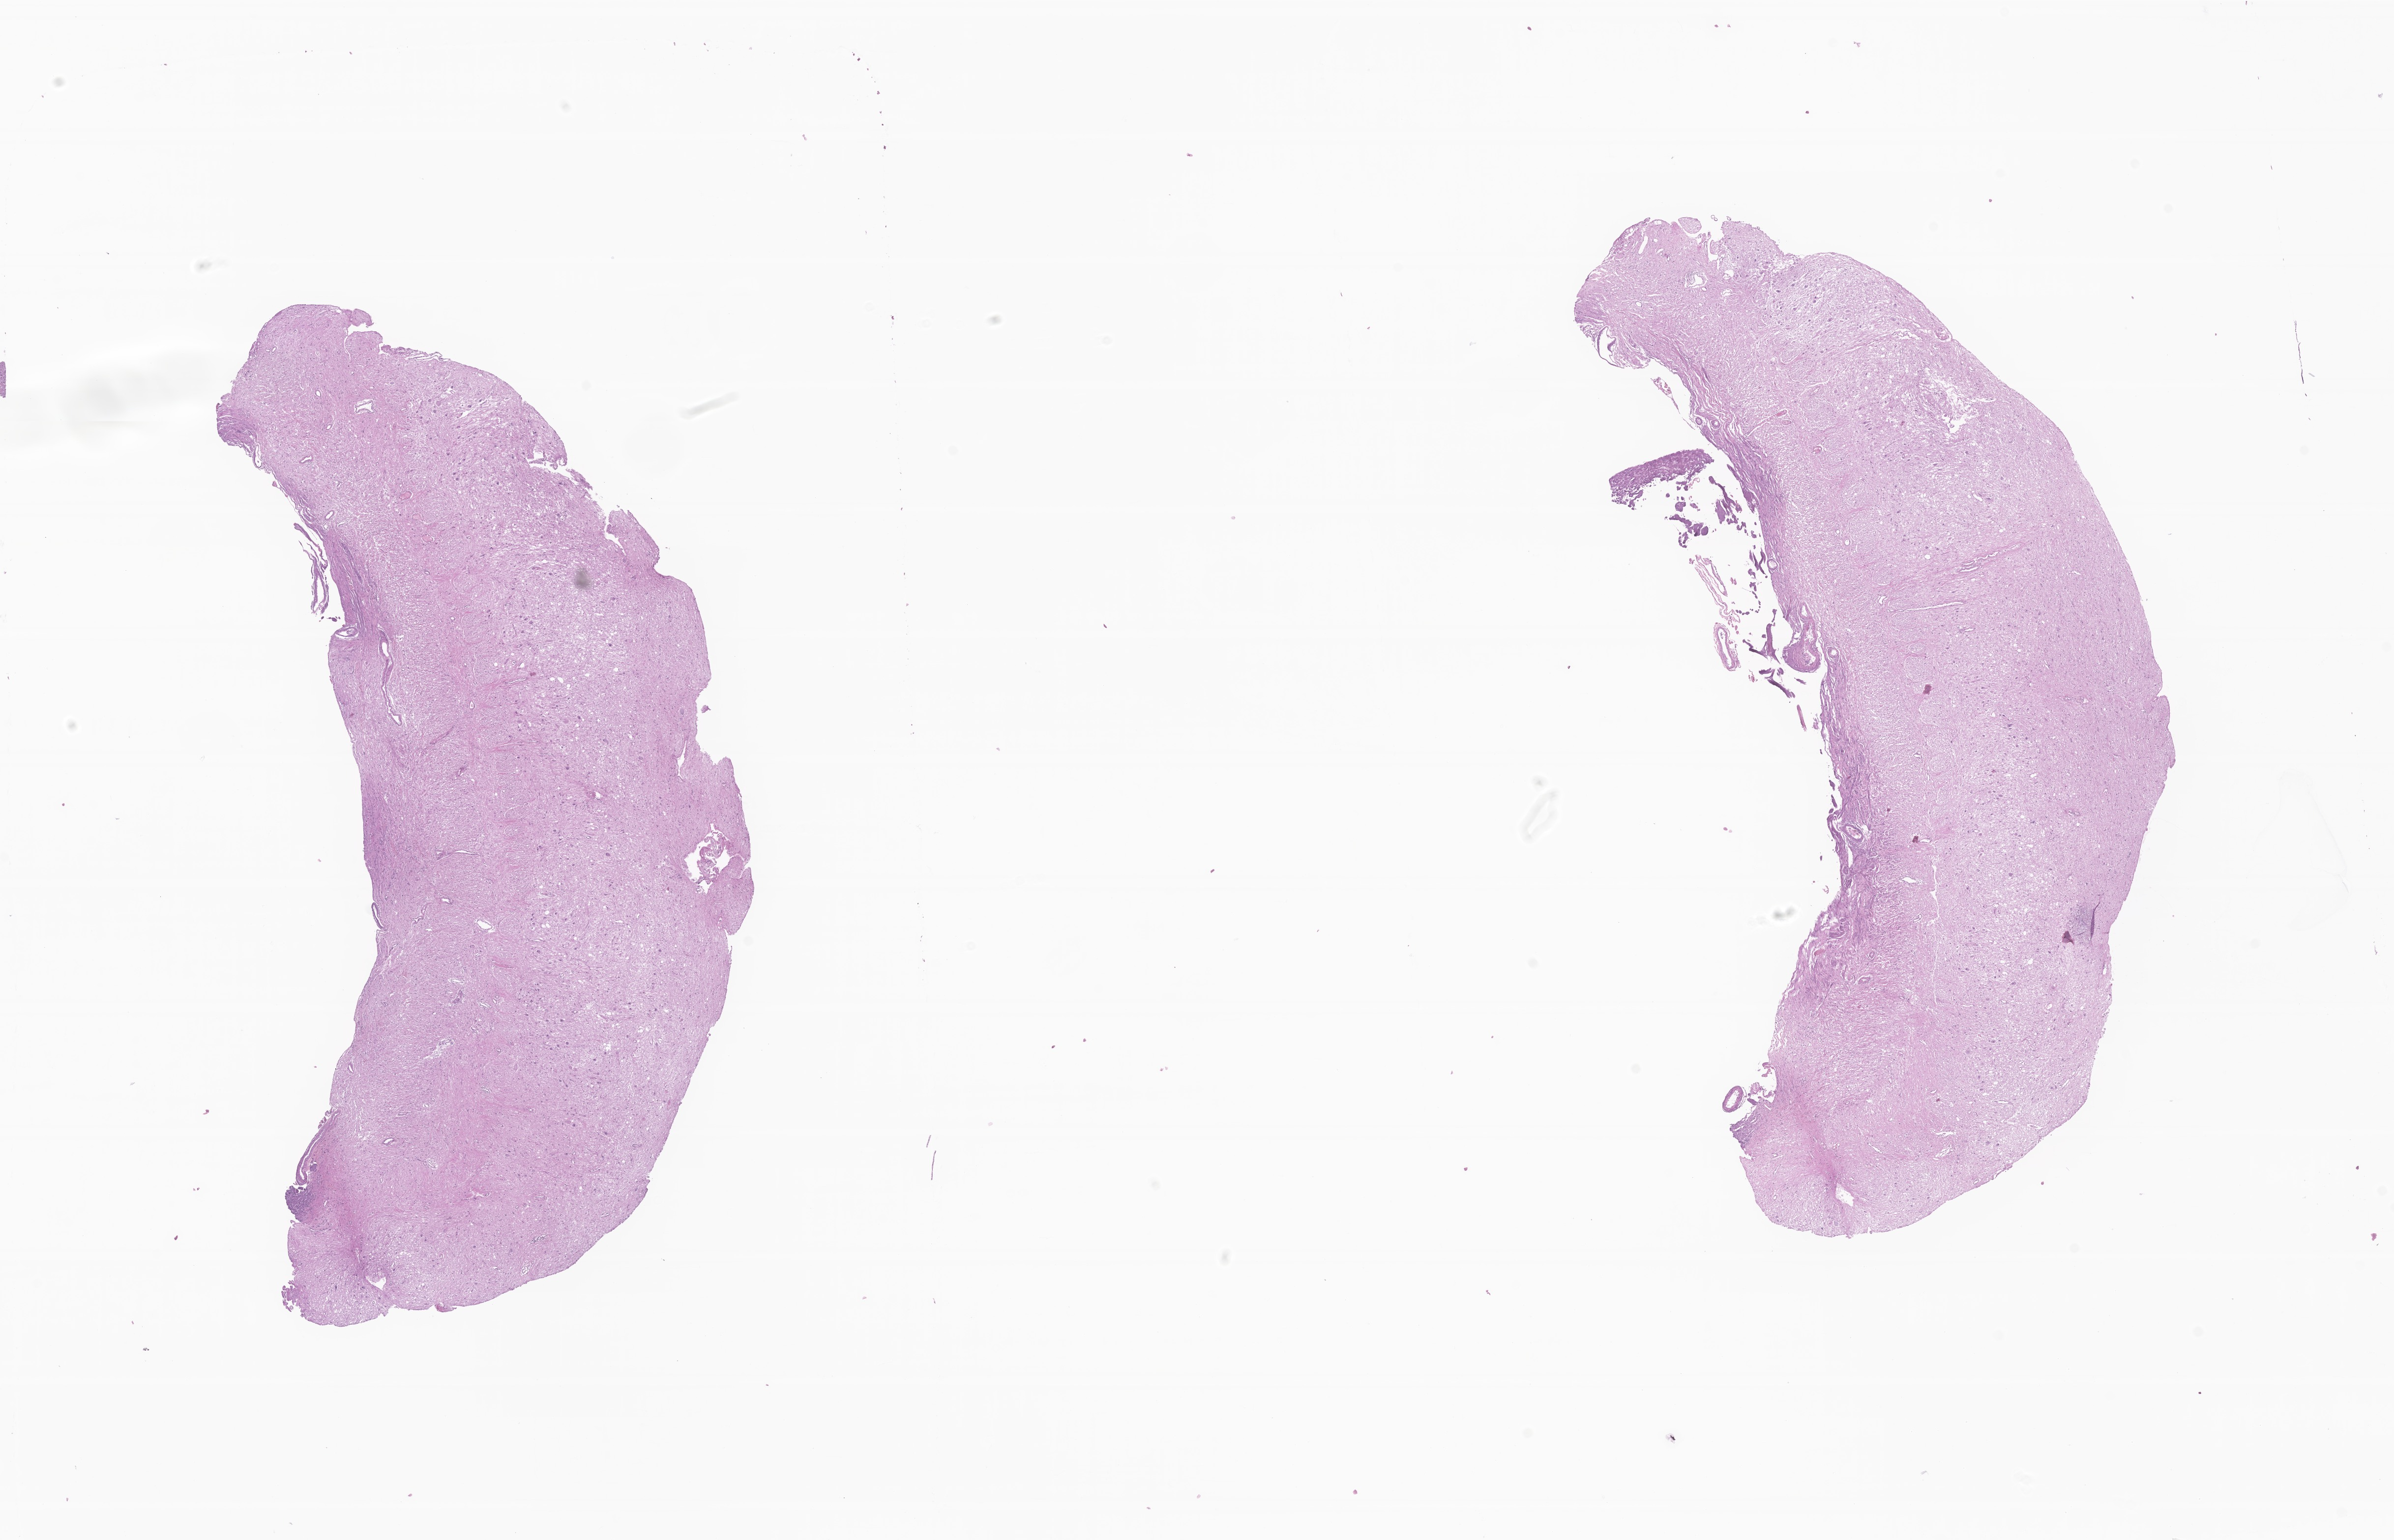
Digitized hematoxylin and eosin (H&E)-stained section of tumor tissue from the spinal cord, whole scanned area (about 20.5 x 13.2 mm) shown as a low-resolution overview. Formalin-fixed, paraffin-embedded (FFPE) tissue. Male patient, age 184 months.
Recorded diagnosis: Ganglioglioma, NOS.